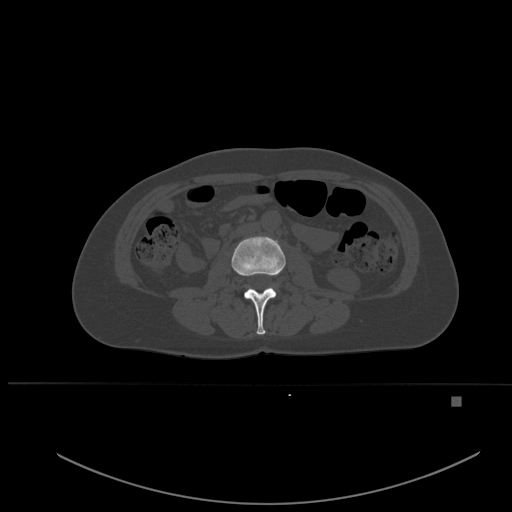
CT including the spine, one axial slice; bone window (W 1800 / L 400 HU); 512 × 512 image matrix, field of view 443 × 443 mm. Female patient, age 49 years. From the clinical record (not read from this slice): primary cancer: breast.
Structures marked on this image (semi-automatic segmentation, software-assisted and operator-edited):
- L2 vertebra: box from (x=231, y=236) to (x=286, y=335) px